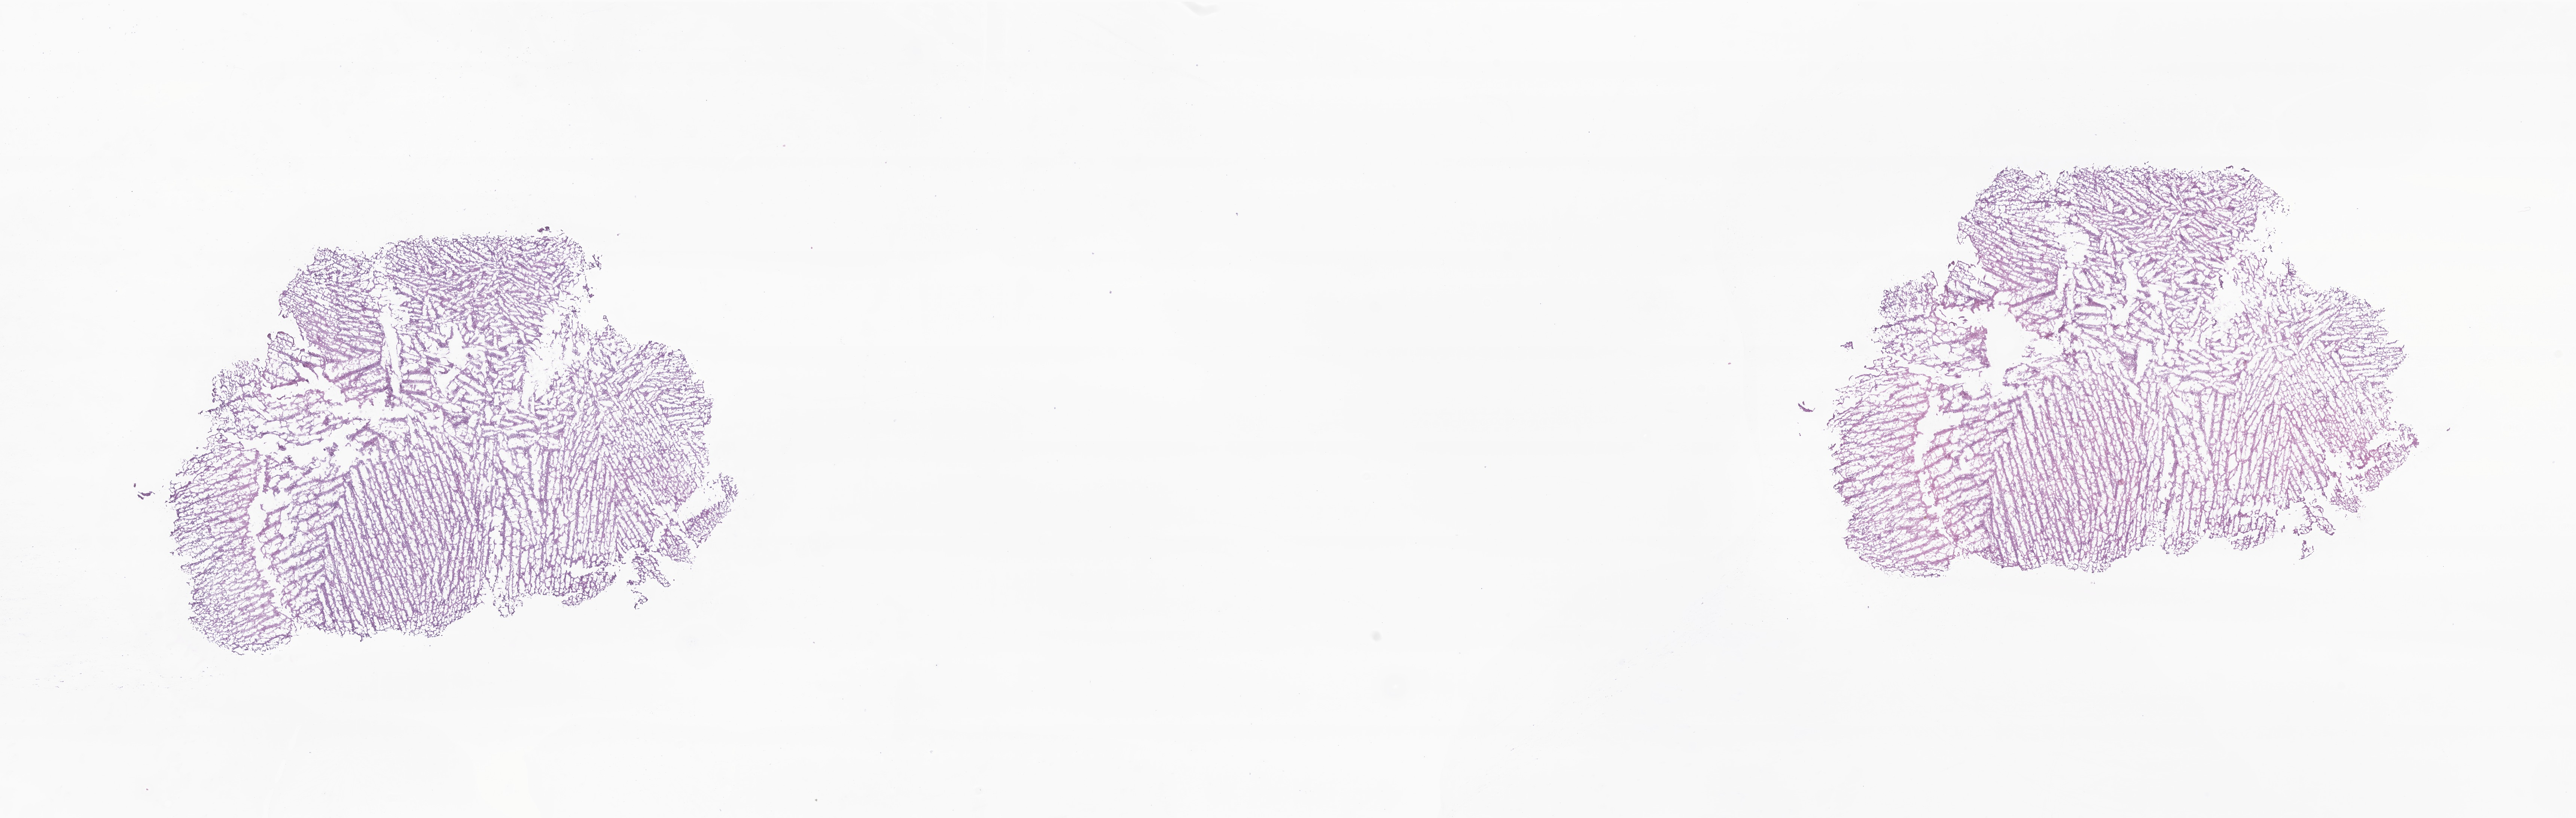
Hematoxylin and eosin (H&E) whole-slide image of tumor tissue from the brain — whole scanned area (about 29.0 x 9.2 mm) shown as a low-resolution overview. Frozen section. Male patient, age 51 months (4 years 3 months).
Diagnosis: Ependymoma, NOS.